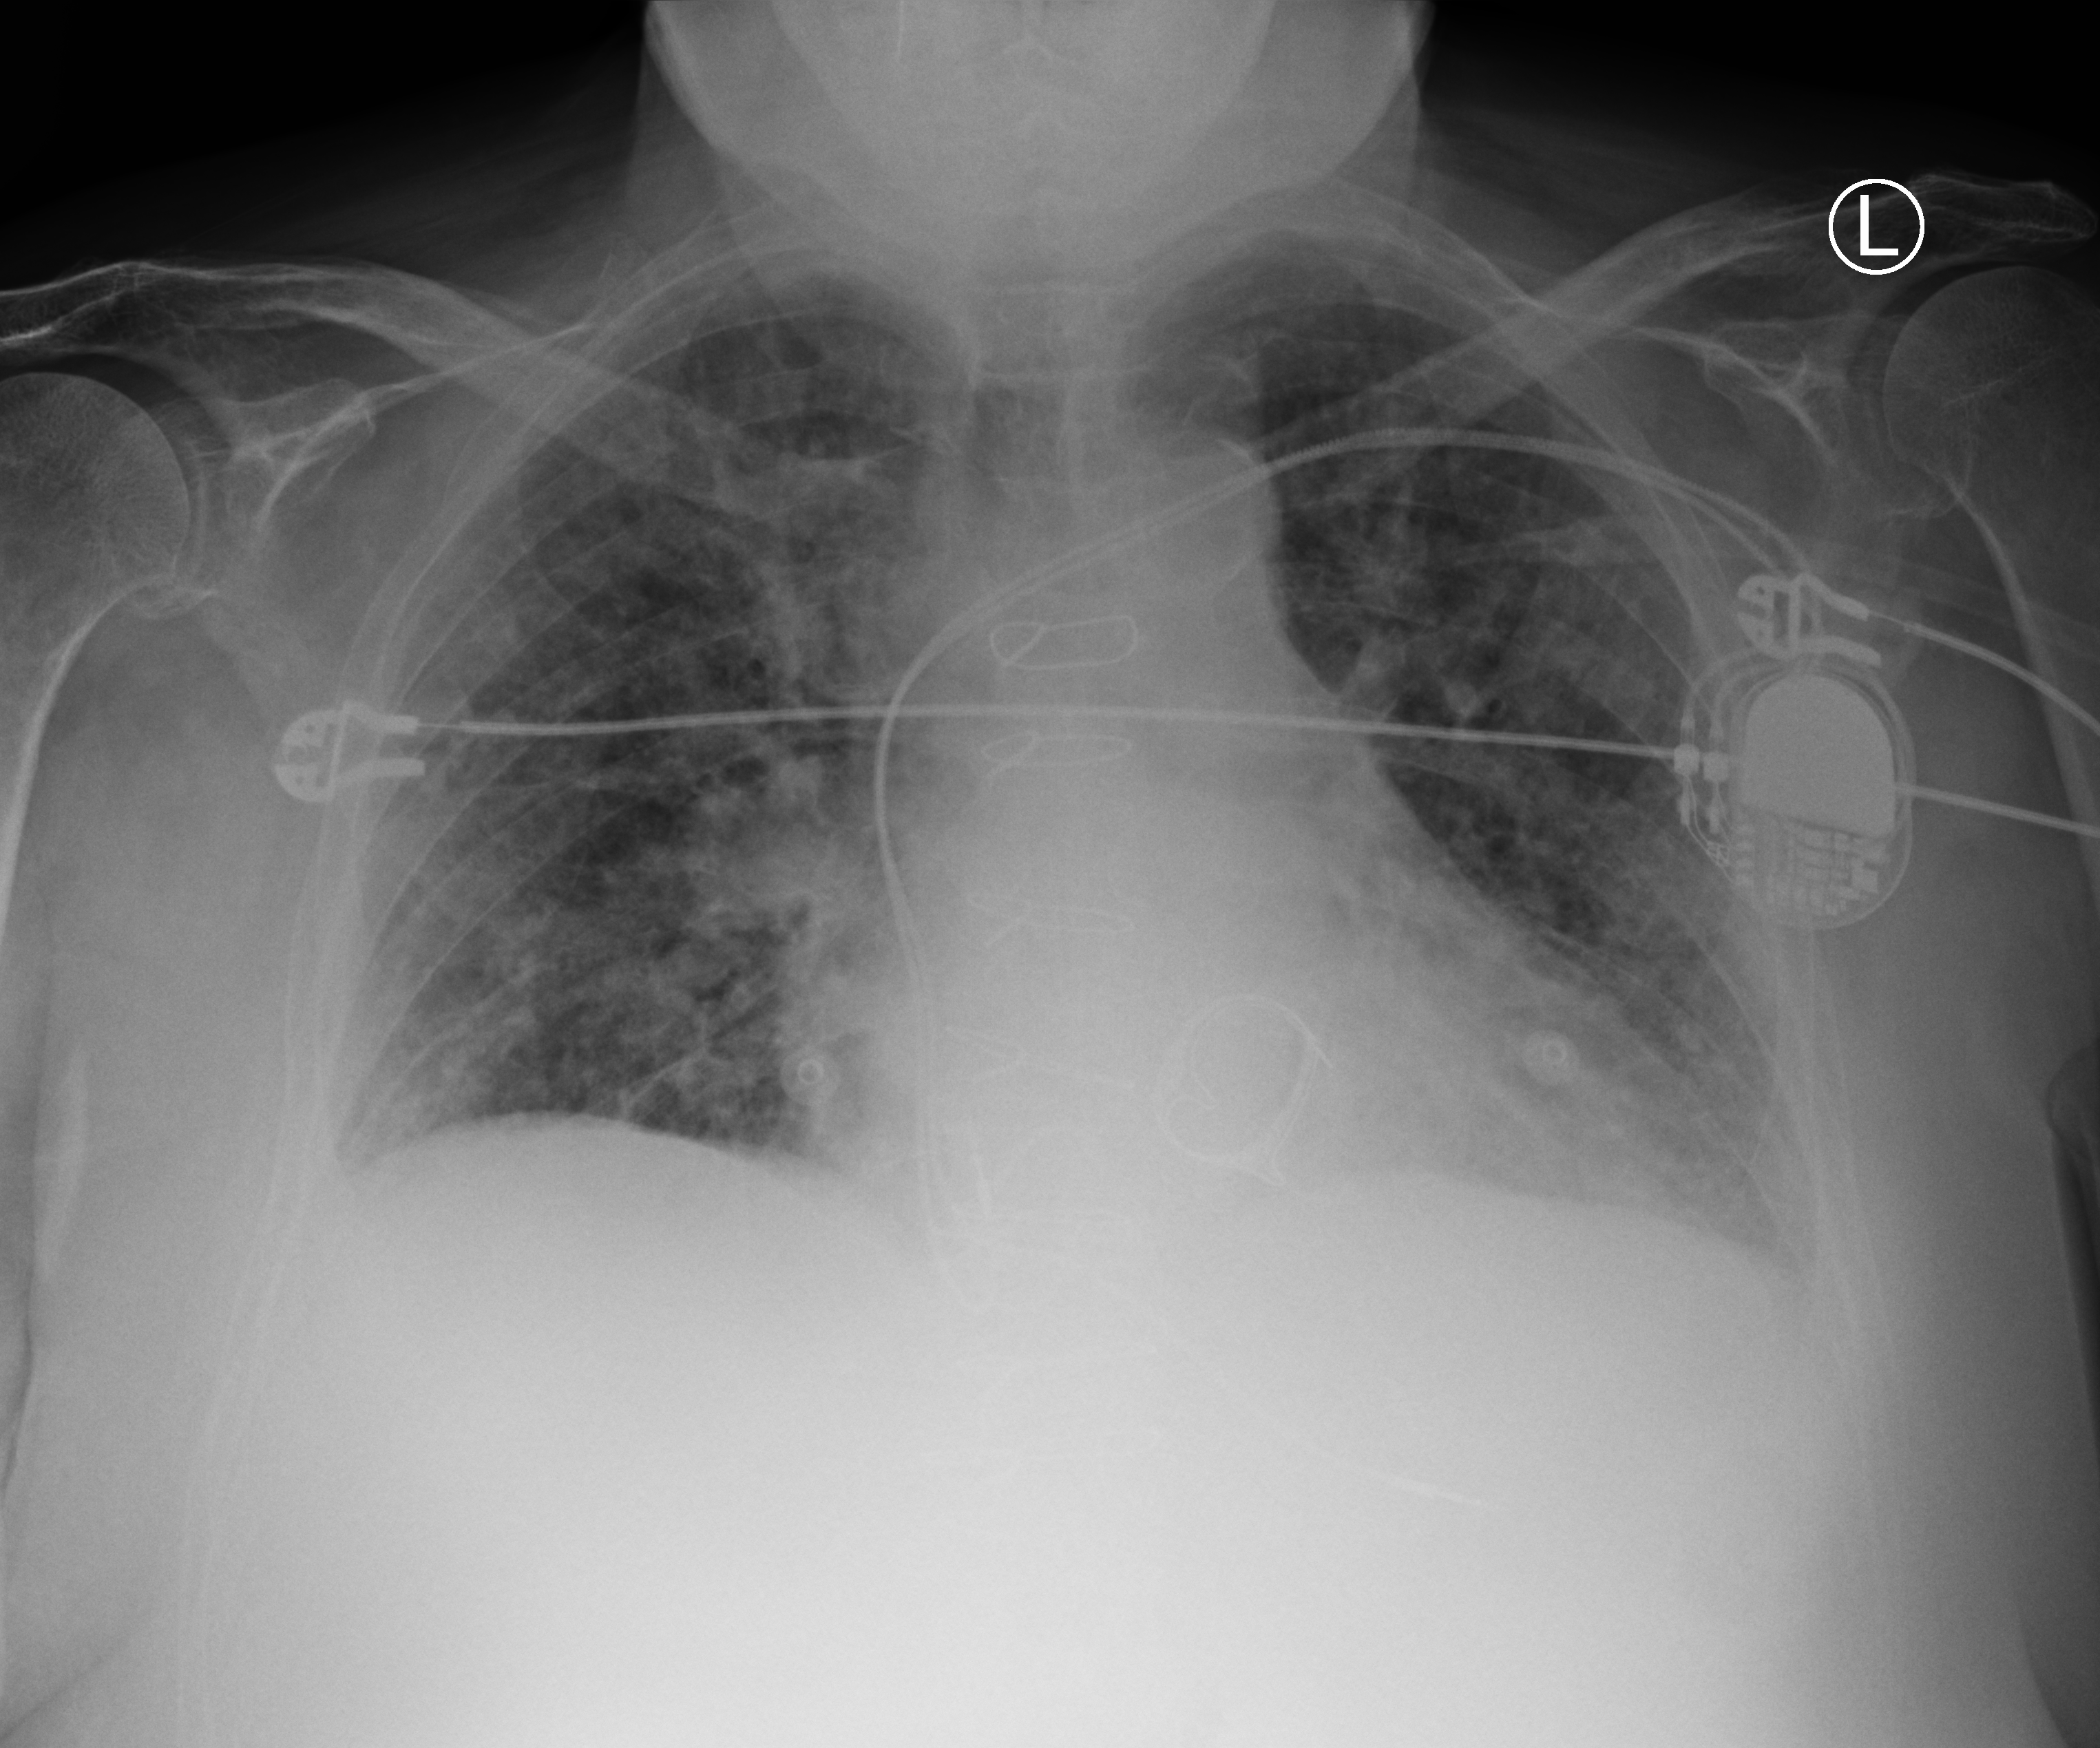
Chest X-ray (portable). Male patient hospitalised with COVID-19, age 75–90 years.
Admission-level facts for this patient (not findings on this image; timing relative to this image not recorded):
- mechanically ventilated during this hospital stay: no
- admitted to intensive care during this hospital stay: no